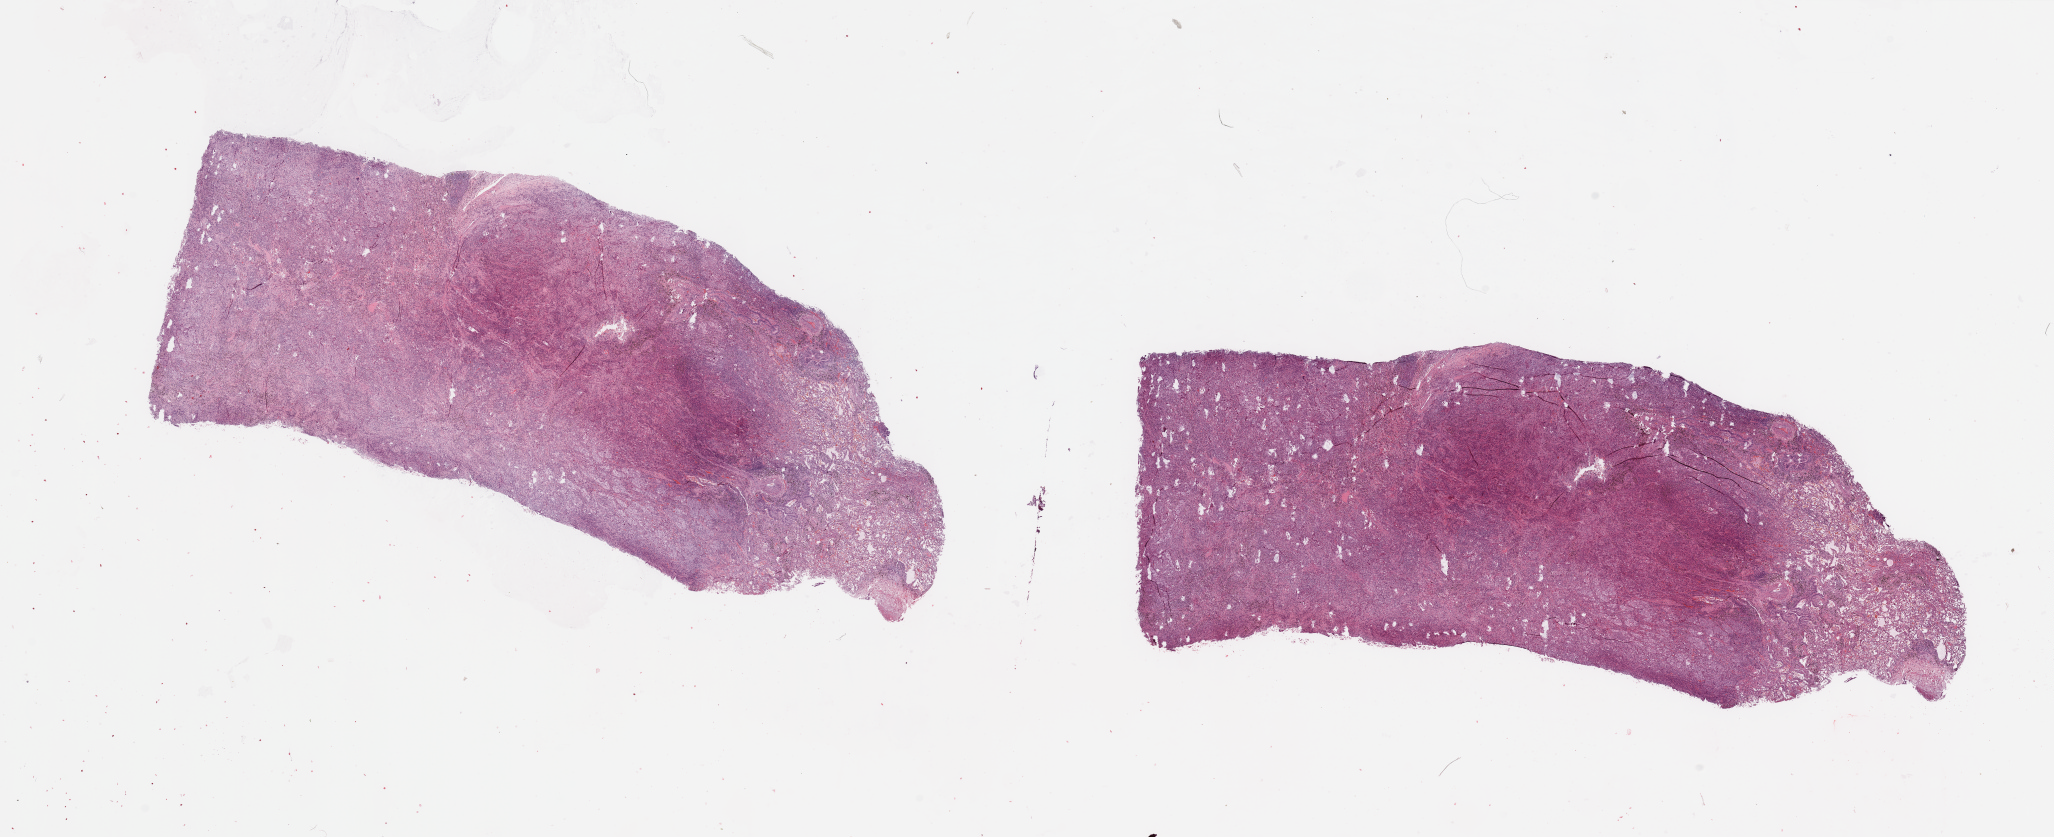
Whole-slide histology image, H&E-stained, low-resolution overview of the scanned area, about 32.5 x 13.2 mm (slide scanned at 20x); tumour tissue sample, sampled site: lung. Male, 65 y/o. Histologic grade: G3 (poorly differentiated). Pathologist review of this section (percent, as recorded): tumour nuclei 75%, necrosis 3%.
• AJCC pathologic stage: IIIA
• diagnosis: Adenocarcinoma, NOS